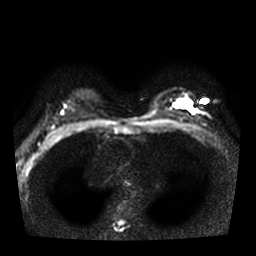
Breast MRI, one axial slice; position 22 of 36 along the scan axis; diffusion-weighted series; image 2 of 4 stored at this slice position (different b-values; order by instance number); 3 T; 5 mm slice thickness; 256 × 256 image matrix, field of view 320 × 320 mm. Female patient.
Structures marked on this image (outlined manually by an expert reader):
- tumour on diffusion-weighted imaging: bounding box [x1, y1, x2, y2] px = [179, 100, 194, 112]